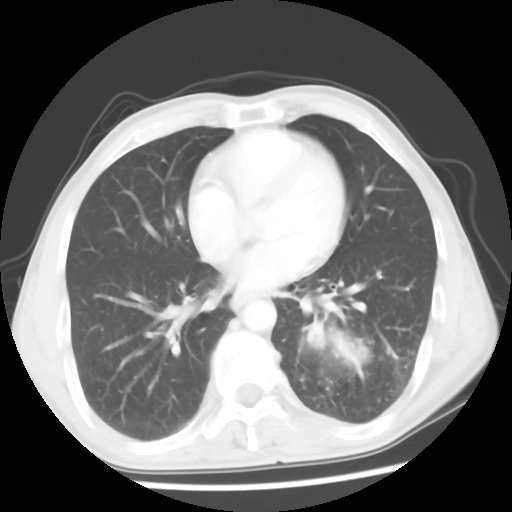
Chest CT, one axial slice. Position 24 of 56 along the scan axis. Reconstruction kernel STANDARD. 120 kVp. Lung window (W 1500 / L -600 HU). 512 × 512 image matrix, field of view 318 × 318 mm. Male patient, age 60 years. Case-level facts recorded for this patient, not image findings: clinical TNM (as recorded): T4 N0 M0.
Outlined on this slice (bounding box drawn by a radiologist):
- lung tumour (recorded histology: squamous cell carcinoma): bounding box [x1, y1, x2, y2] px = [303, 313, 370, 383]